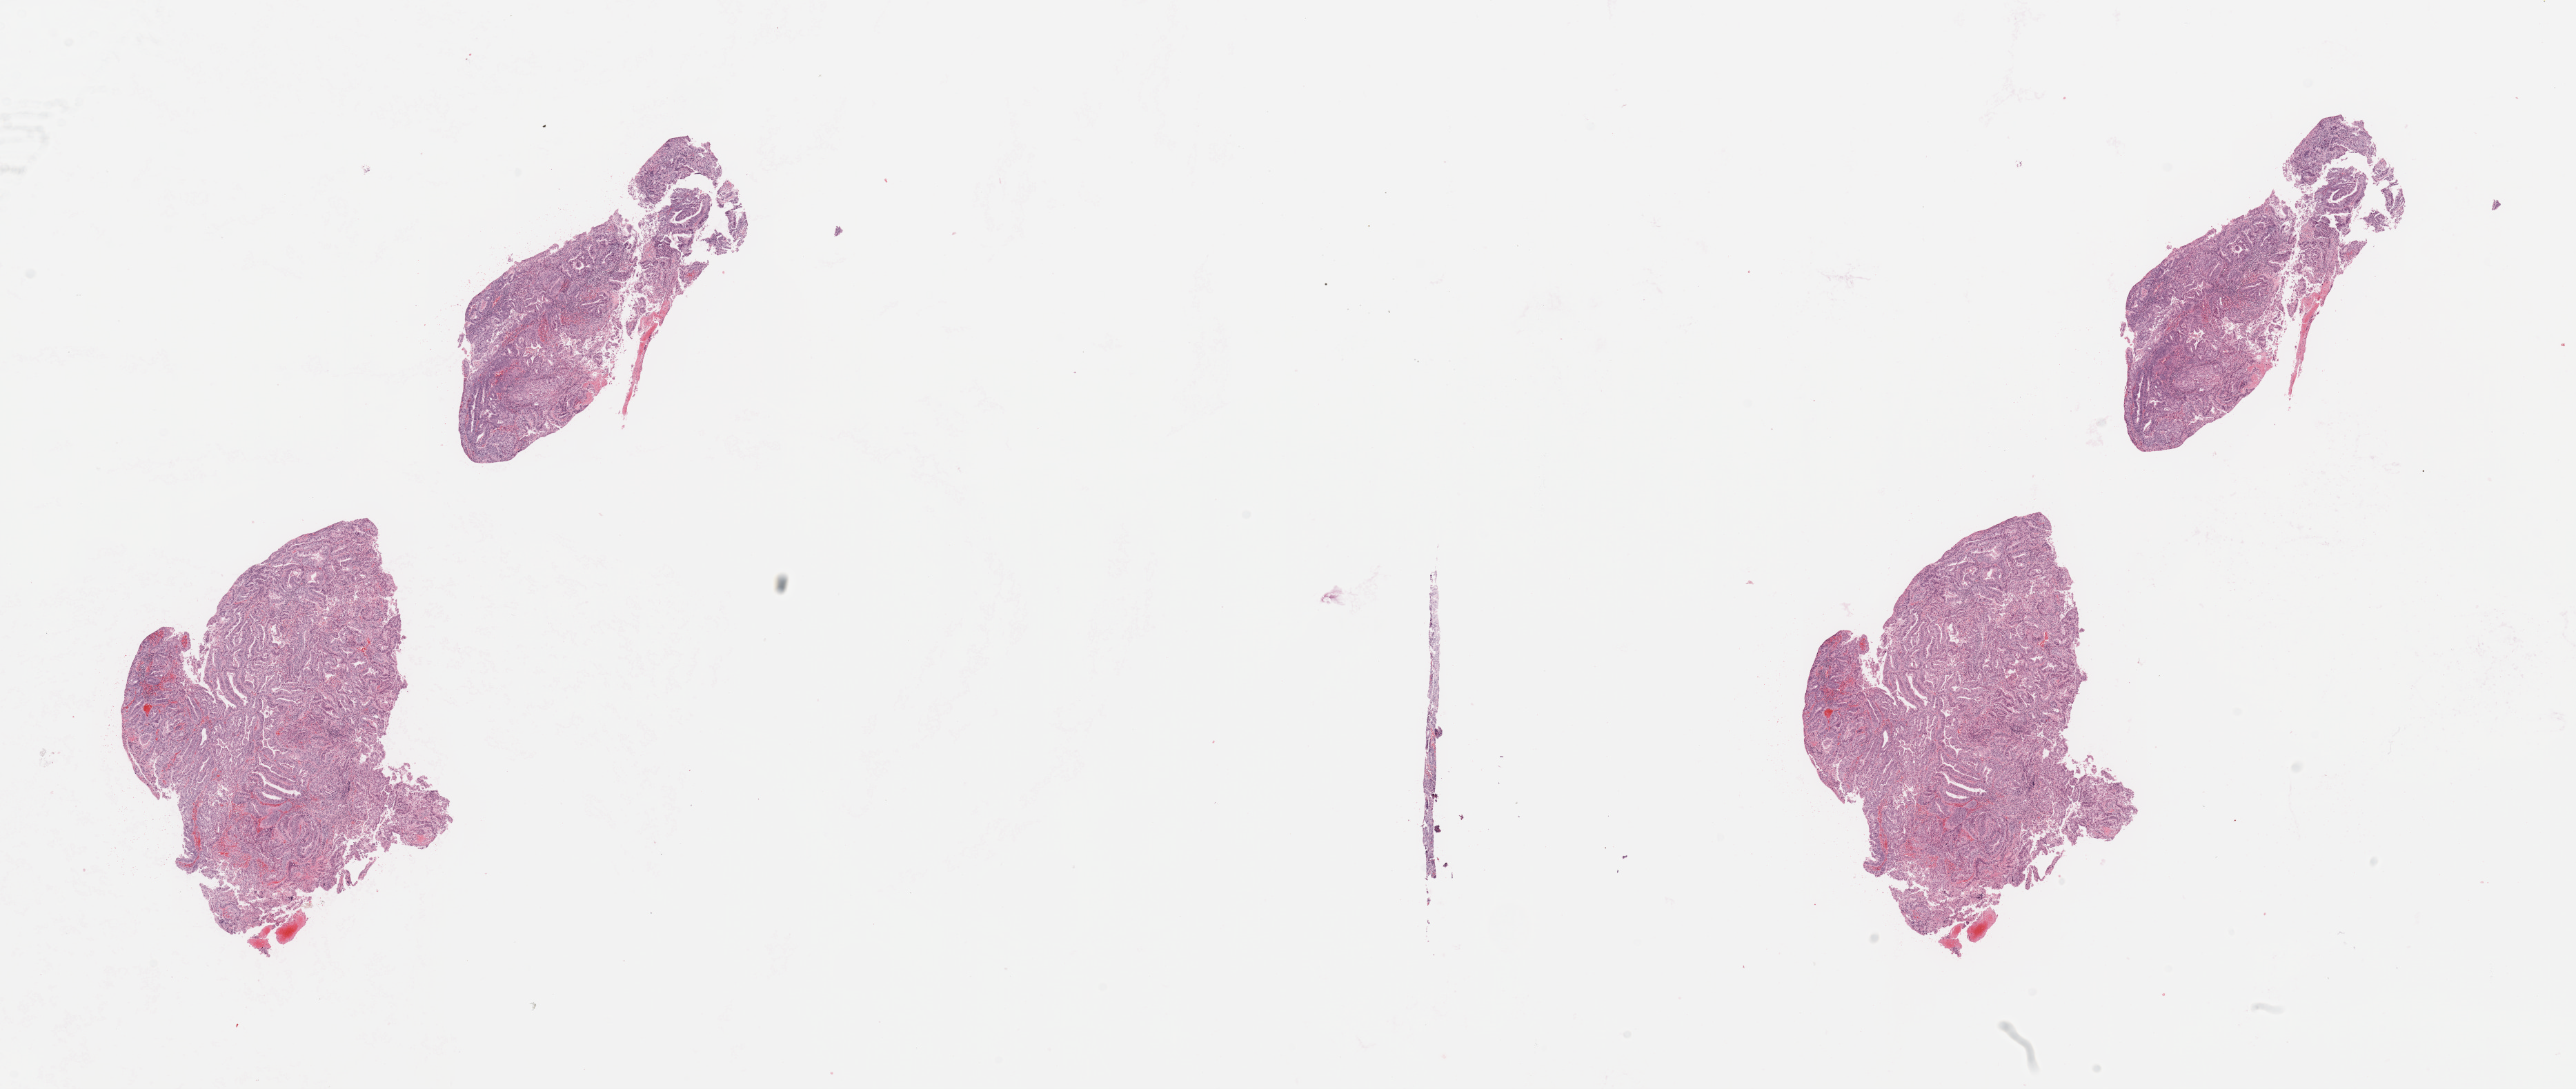
Whole-slide histology image, Hematoxylin and eosin (H&E) stained — a low-resolution overview of the entire scanned area, about 29.5 x 12.5 mm (acquisition: 20x scan). Tumour tissue sample, sampled site: uterus. Female, 69 y/o. Pathologist review of this section (percent, as recorded): tumour nuclei 85%, necrosis 2%.
Diagnosis: Endometrioid adenocarcinoma, NOS.